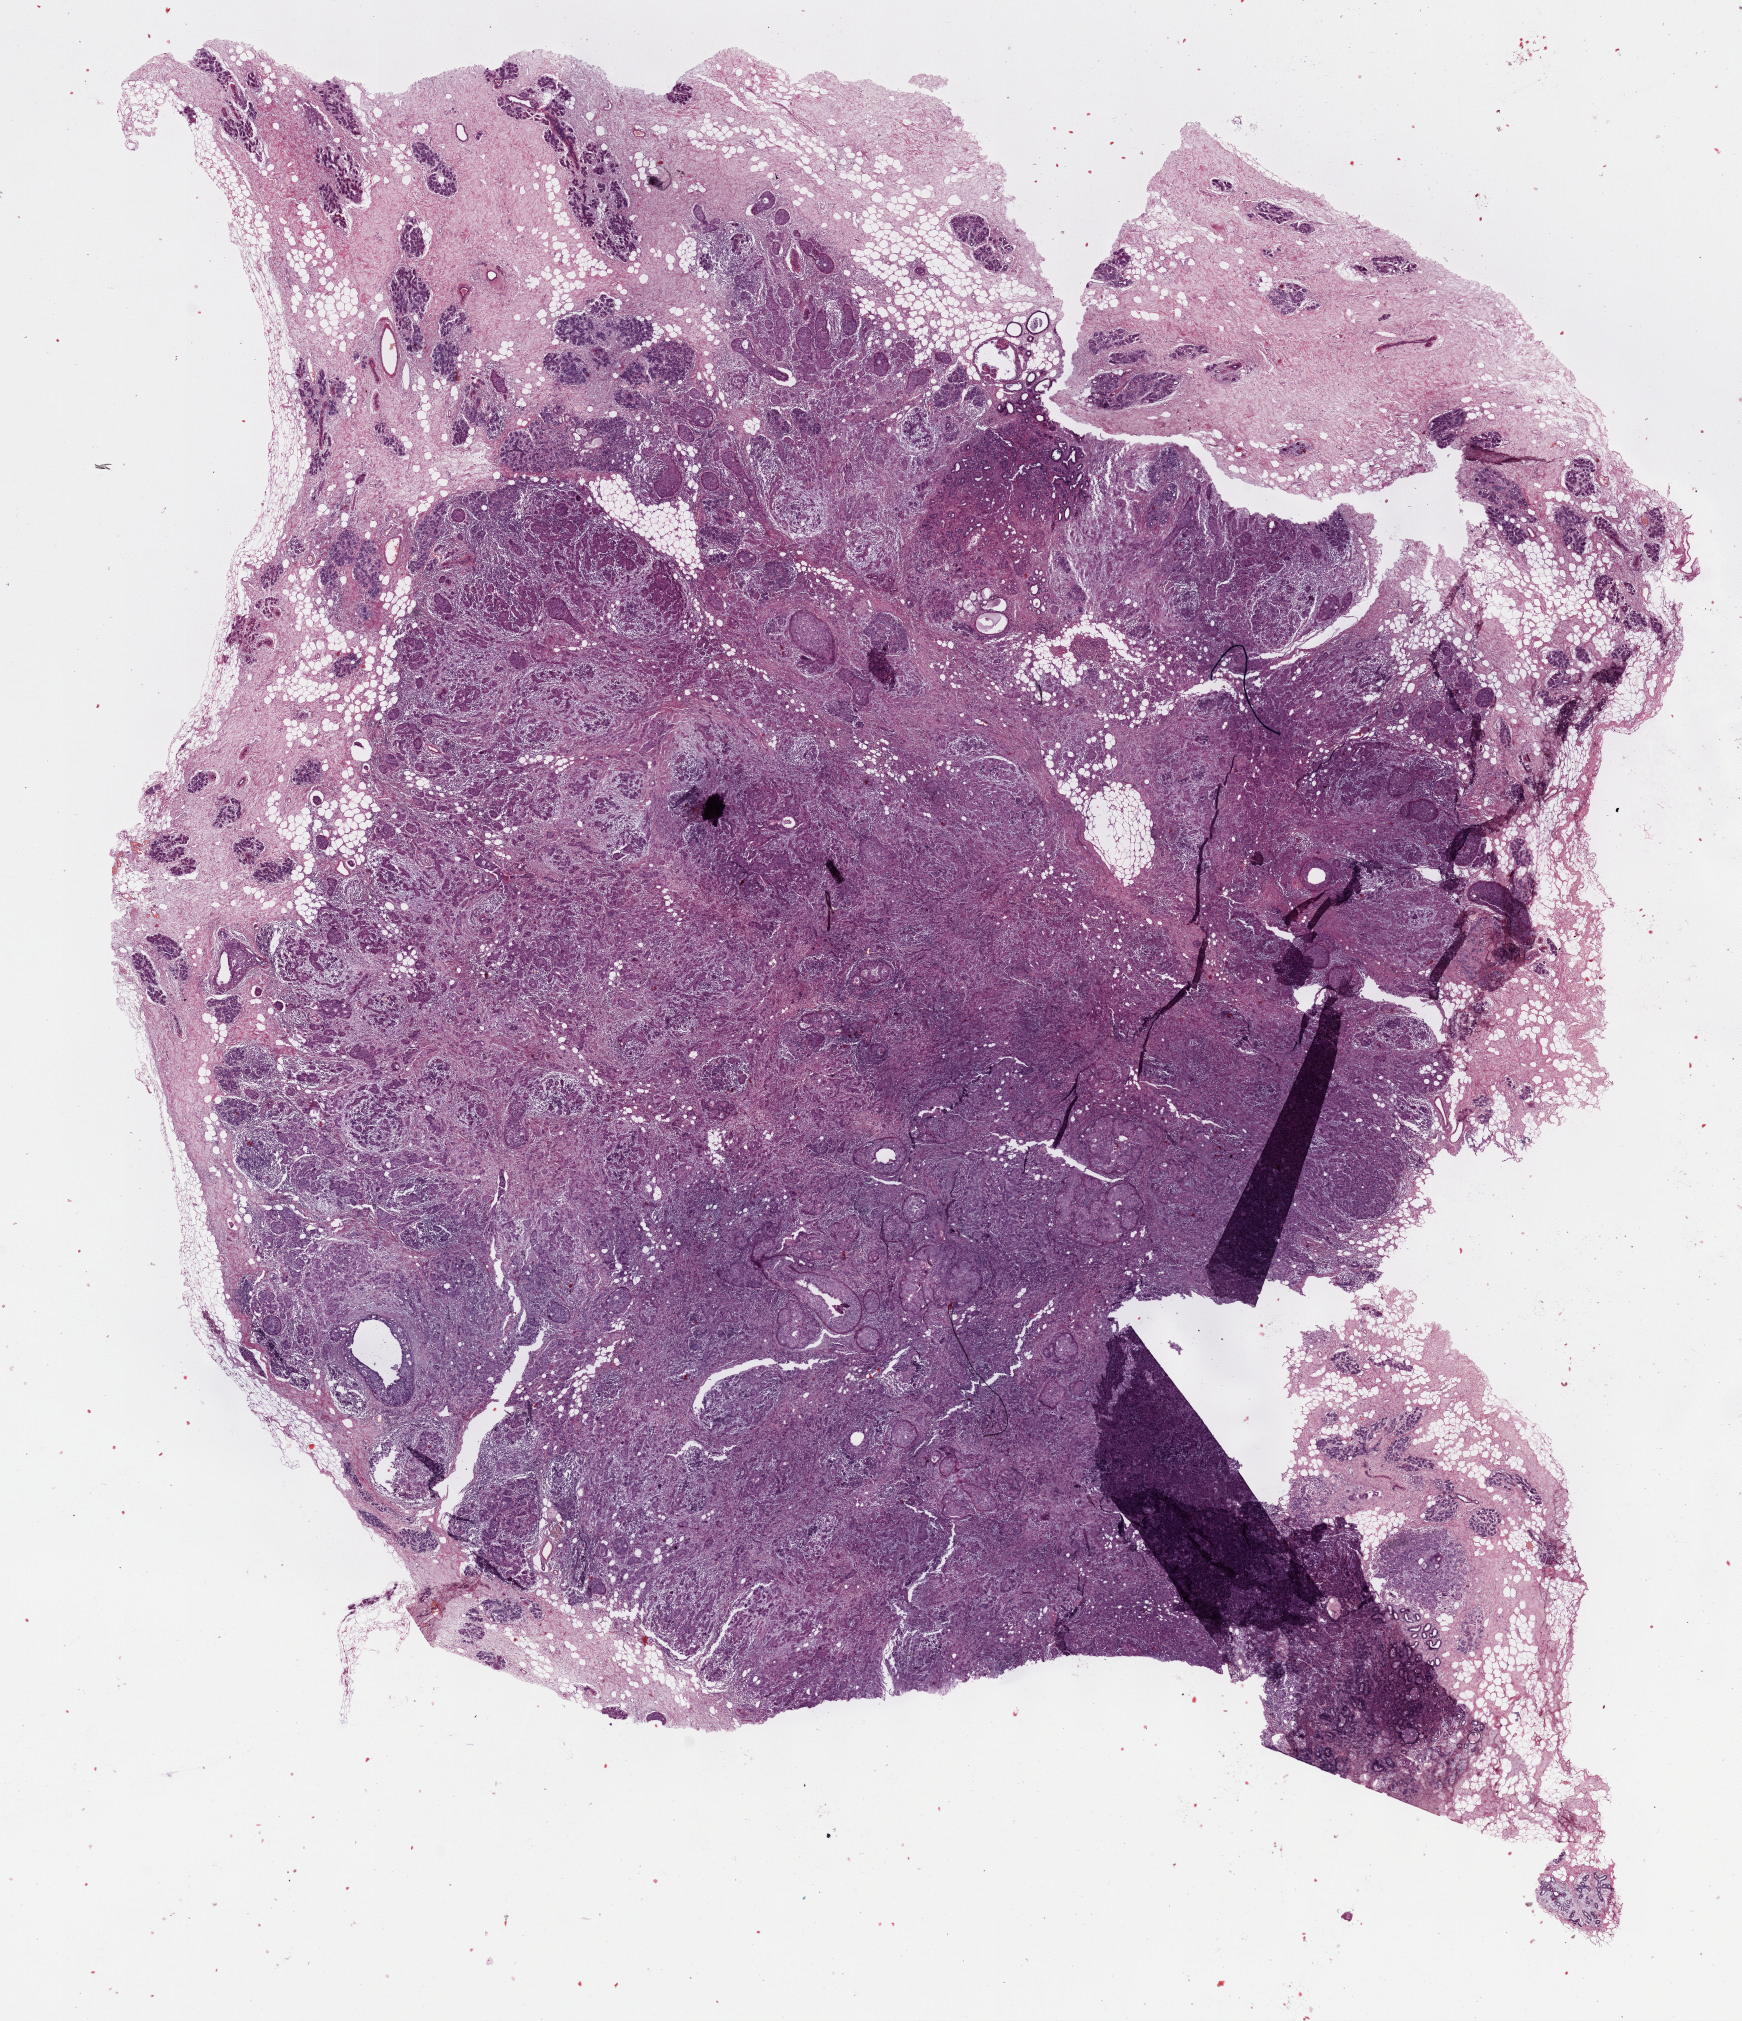
Whole-slide histology image, Hematoxylin and eosin (H&E) stained — whole scanned area (about 14.1 x 16.4 mm) shown as a low-resolution overview. FFPE section. Breast, primary tumour sample. Patient: female, age at initial diagnosis 40 years.
Diagnosis: Infiltrating duct carcinoma, NOS. Lymph nodes positive (case pathology): 1 of 15 examined.